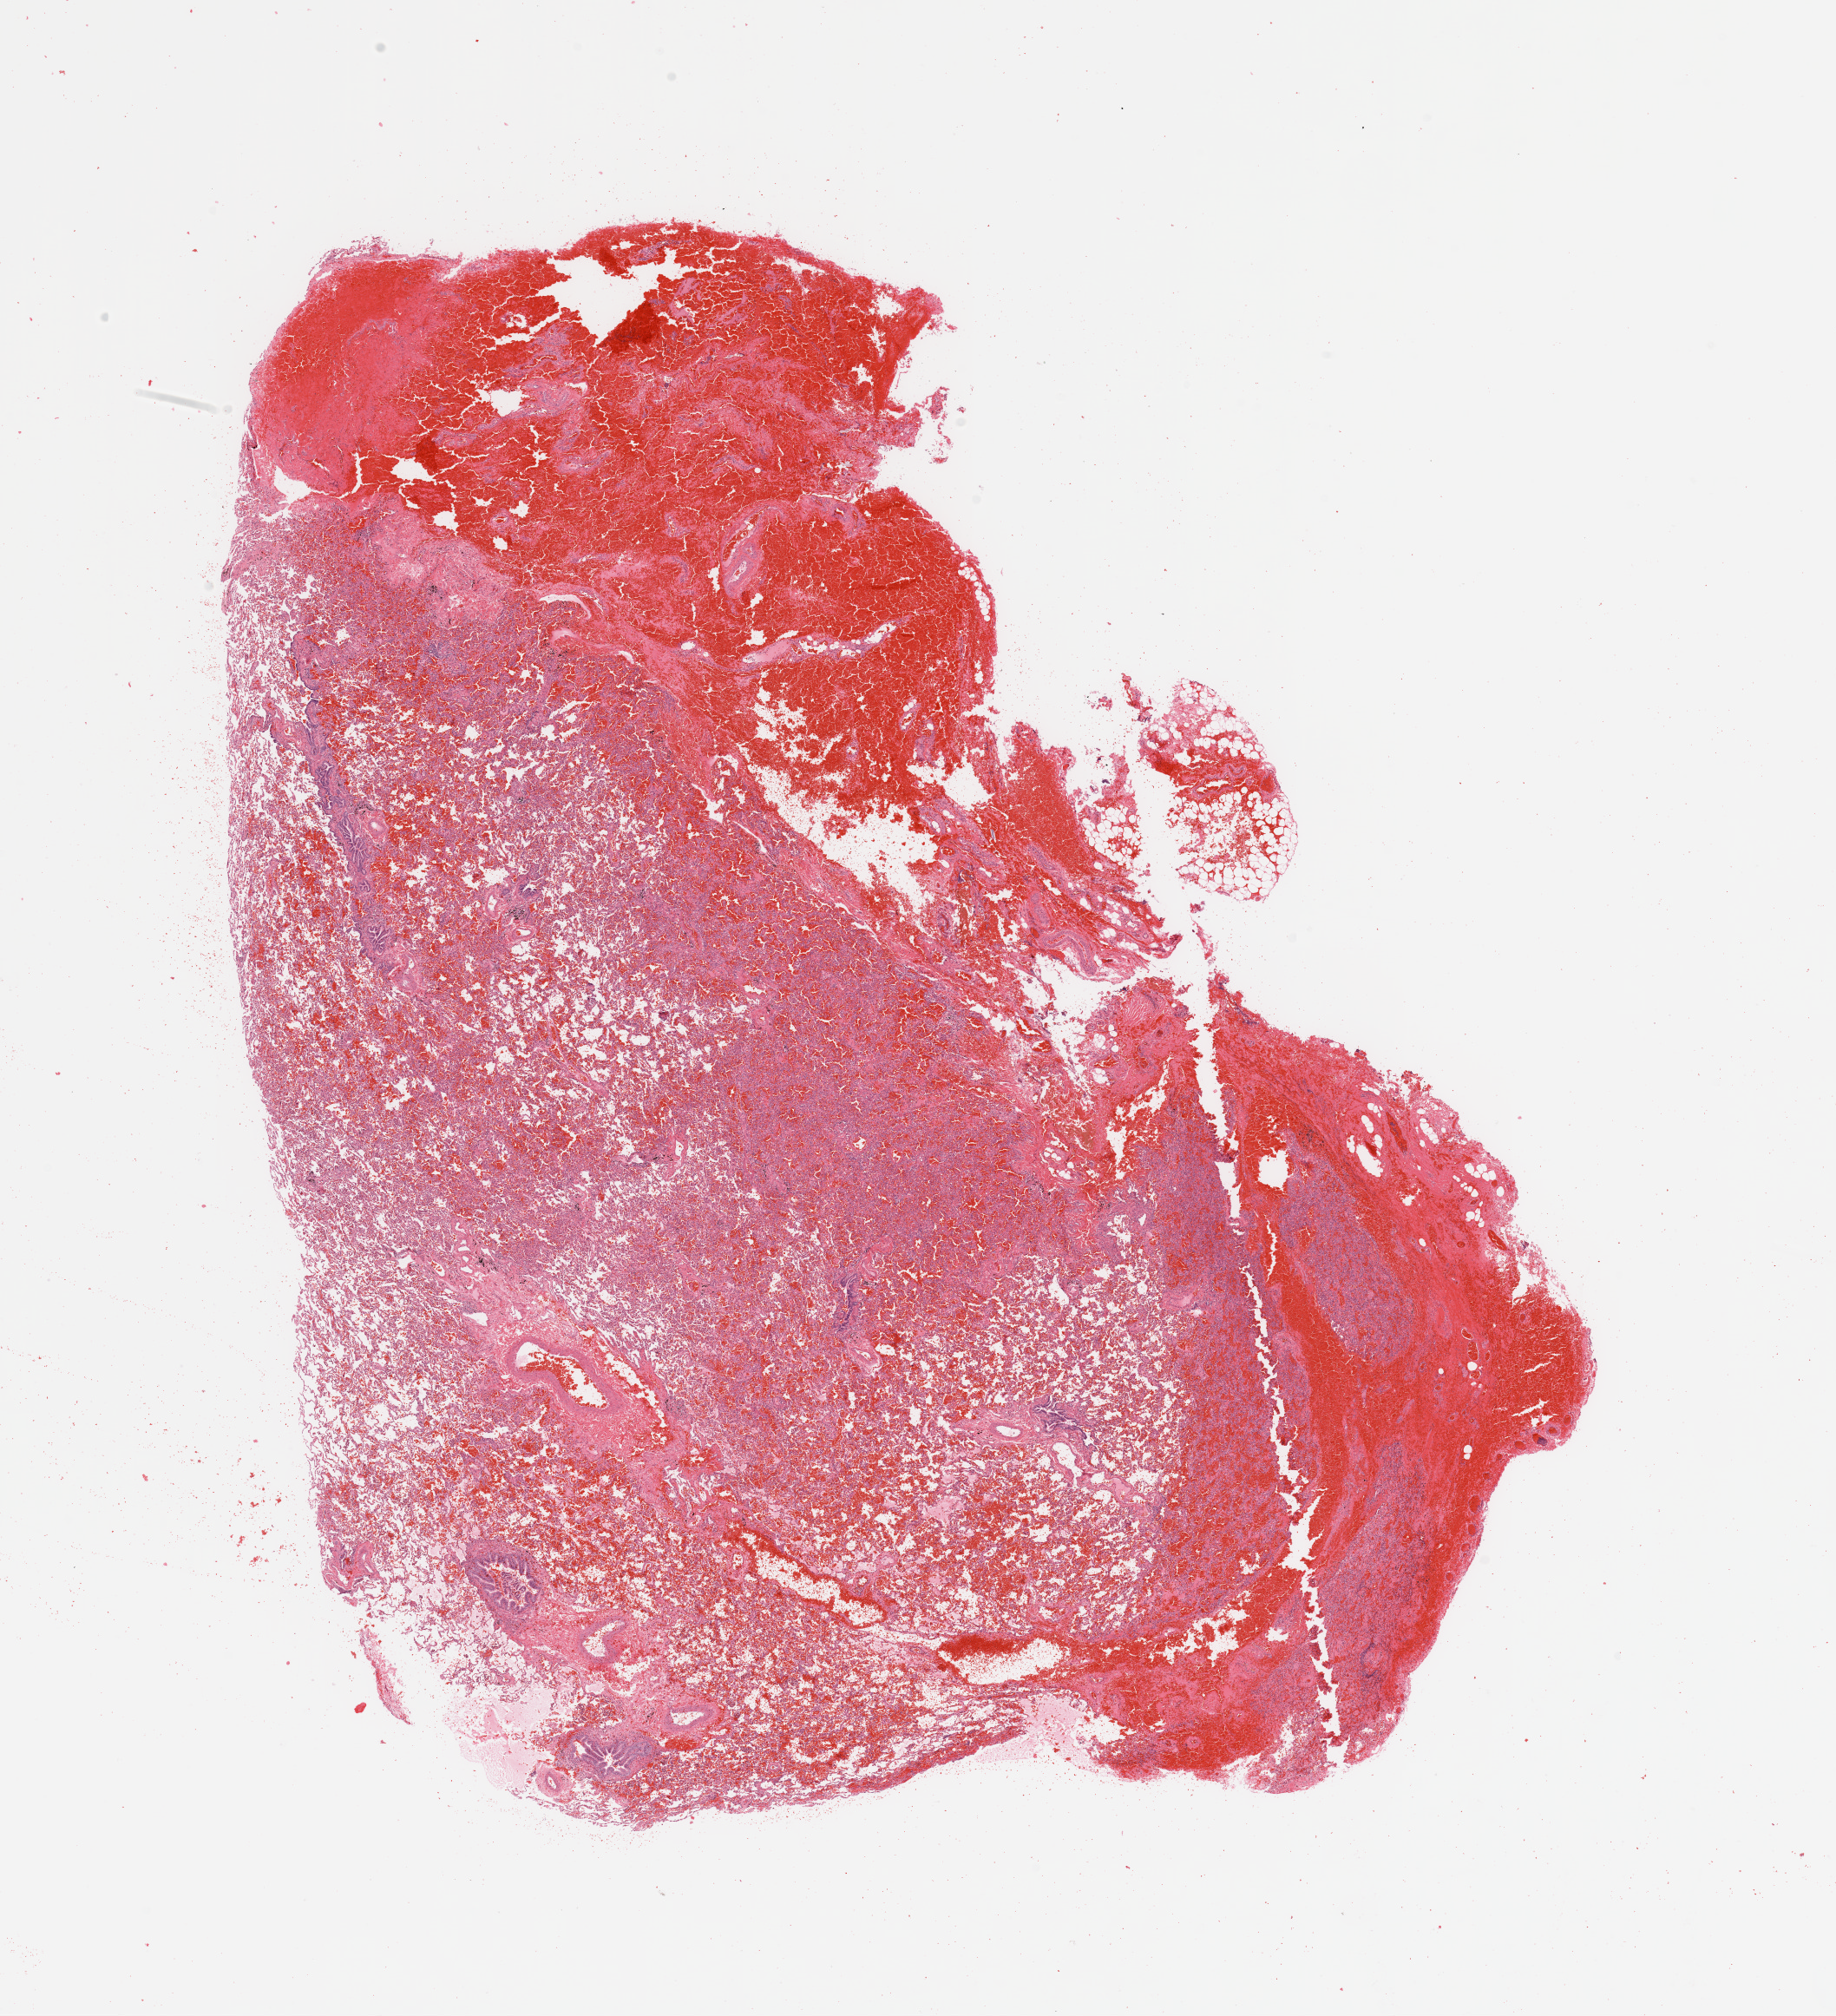
Hematoxylin and eosin (H&E) stained whole-slide image, shown as a low-resolution overview of the whole scanned area (about 16.7 x 18.4 mm, from a 20x scan), normal (non-tumour) tissue sample, sampled site: lung. Patient: male, age 40 years.
• this section: normal (non-tumour) tissue from the same patient
• patient diagnosis: Adenocarcinoma, NOS